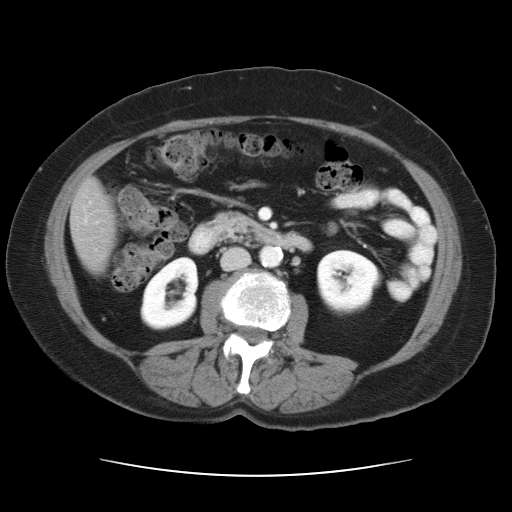
Contrast-enhanced abdominal CT, one axial slice; position 9 of 34 along the scan axis; reconstruction kernel STANDARD; intravenous contrast given; soft-tissue window (W 400 / L 40 HU); 512 × 512 image matrix, field of view 360 × 360 mm. Female patient, age 65 years. From the clinical record (not read from this slice): diagnosis: colorectal cancer liver metastases, imaged before liver resection; multiple liver metastases: yes; largest metastasis: 2.2 cm; disease in both lobes: no.
Outlined on this slice (manually delineated by an expert):
- liver: bounding box [x1, y1, x2, y2] px = [73, 183, 114, 265]
- planned liver remnant (the part of the liver to remain after resection): [73, 183, 114, 264]